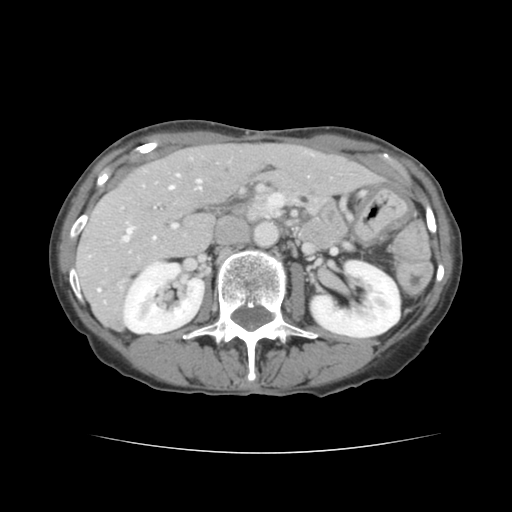
Contrast-enhanced abdominal CT, one axial slice; intravenous contrast given; soft-tissue window (W 400 / L 40 HU); 2.5 mm slice thickness; 512 × 512 image matrix, field of view 319 × 319 mm. Female patient, age 77 years. Case-level facts recorded for this patient, not image findings: diagnosis: colorectal cancer liver metastases, imaged before liver resection; multiple liver metastases: yes; largest metastasis: 3 cm; disease in both lobes: no.
Structures marked on this image (expert manual segmentation):
- hepatic veins: bounding box (x1, y1, x2, y2) in pixels: (123, 174, 201, 241)
- liver: (77, 144, 378, 328)
- planned liver remnant (the part of the liver to remain after resection): (159, 144, 378, 205)
- portal vein (with intrahepatic branches): (98, 187, 198, 292)